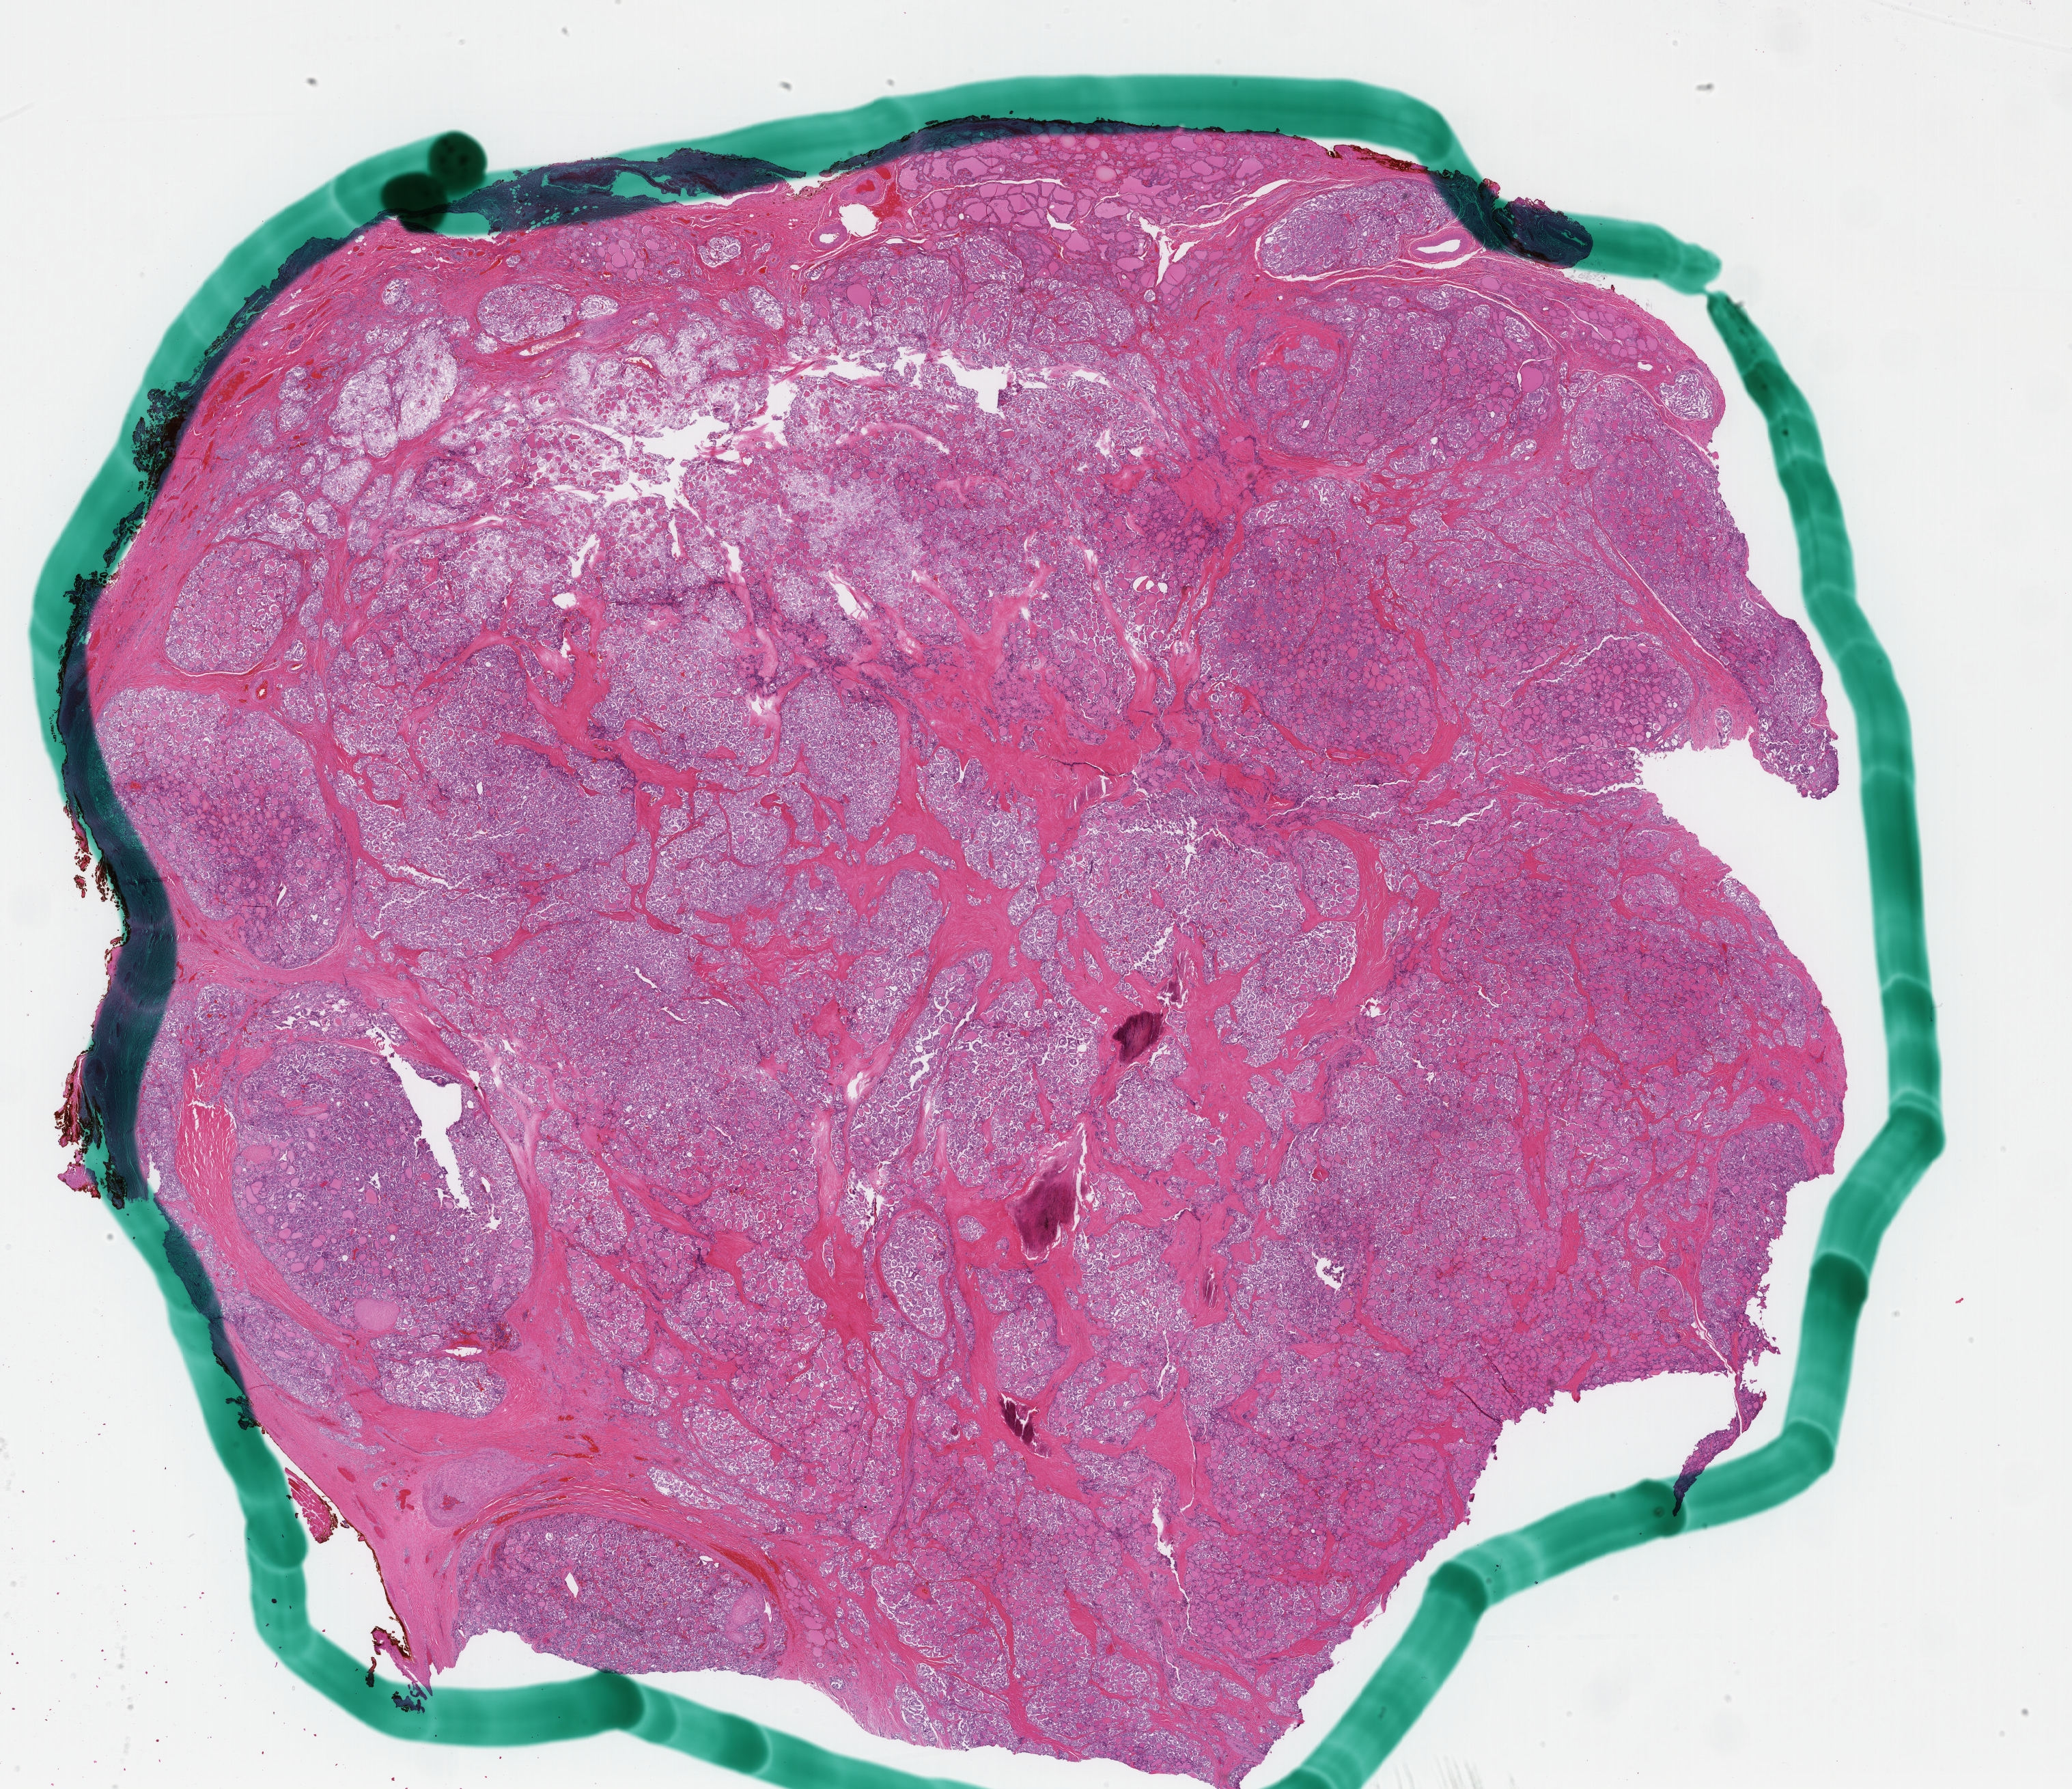
Digitized Hematoxylin and eosin (H&E) stained tissue section (whole slide), shown as a low-resolution overview of the whole scanned area (about 24.1 x 20.8 mm, slide scanned at 40x); formalin-fixed paraffin-embedded (FFPE) diagnostic section; sample: primary tumour, thyroid. Female, age 43 years at initial diagnosis.
TNM: T3 N1b MX. AJCC pathologic stage: I. Histologic diagnosis: Papillary carcinoma, follicular variant (thyroid gland).